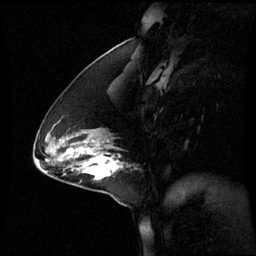
Breast MRI (dynamic contrast-enhanced), one sagittal slice. Position 23 of 60 along the scan axis. Dynamic contrast-enhanced series, image 2 of 3 at this slice position (ordered by acquisition). 1.5 T. TE 4.2 ms, TR 8.9 ms. 2.2 mm slice thickness. 256 × 256 image matrix, field of view 240 × 240 mm. Patient: female, 44 years. From the clinical record (not read from this slice): setting: breast cancer imaged before/during neoadjuvant chemotherapy; receptor status: triple-negative.
Annotated regions visible in this slice (semi-automatically segmented with operator editing):
- analysis volume of interest (the breast-tissue region the enhancement analysis was run in; not a lesion): box from (x=76, y=150) to (x=128, y=181) px
- tumour enhancement mask (voxels above the 70 % enhancement threshold inside the analysis volume of interest): (x=83, y=156)–(x=117, y=181)